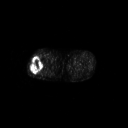
FDG PET of an extremity soft-tissue mass (from a PET/CT study), one axial slice; slice 247 of 267 in the series (ordered by position); 3.27 mm slice thickness; 128 × 128 image matrix, field of view 700 × 700 mm. Patient: male, 43 years. From the clinical record (not read from this slice): histological type: poorly differentiated synovial sarcoma; grade: high; site of the primary tumour: right buttock.
Outlined on this slice (expert contour drawn on MRI and transferred to this co-registered scan by the dataset authors):
- gross tumour volume including surrounding oedema: box from (x=29, y=57) to (x=44, y=74) px
- gross tumour volume (mass): (x=29, y=57)–(x=43, y=74)